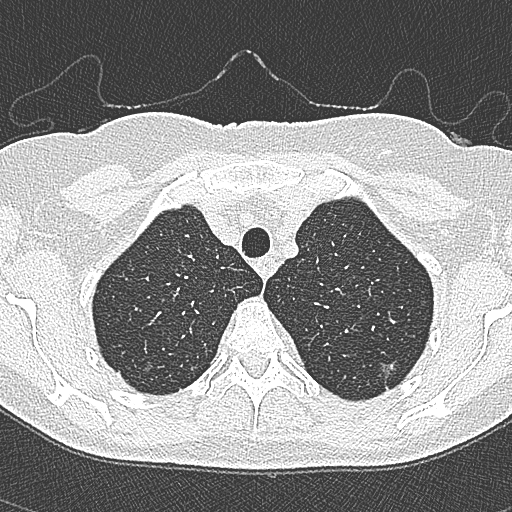
Axial slice from a low-dose chest CT screening exam, second screening round (one year after baseline), lung window (W 1500 / L -600 HU), lung (sharp) reconstruction kernel (B80f), slice 49 of 350 in the series, 512 × 512 image matrix. Female participant, aged 65 years at enrolment.
Expert-annotated lung lesion, bounding box <368,346,412,388> (left, top, right, bottom; pixels). The screening reader recorded 4 non-calcified nodules or masses ≥4 mm on this exam (left upper lobe, left upper lobe, left upper lobe, right lower lobe); which of them this box marks is not recorded. Participant outcome: lung cancer diagnosed 54 days after this screen — bronchiolo-alveolar carcinoma, non-mucinous, left upper lobe, stage IA (AJCC 6th edition), 10 mm at pathology.